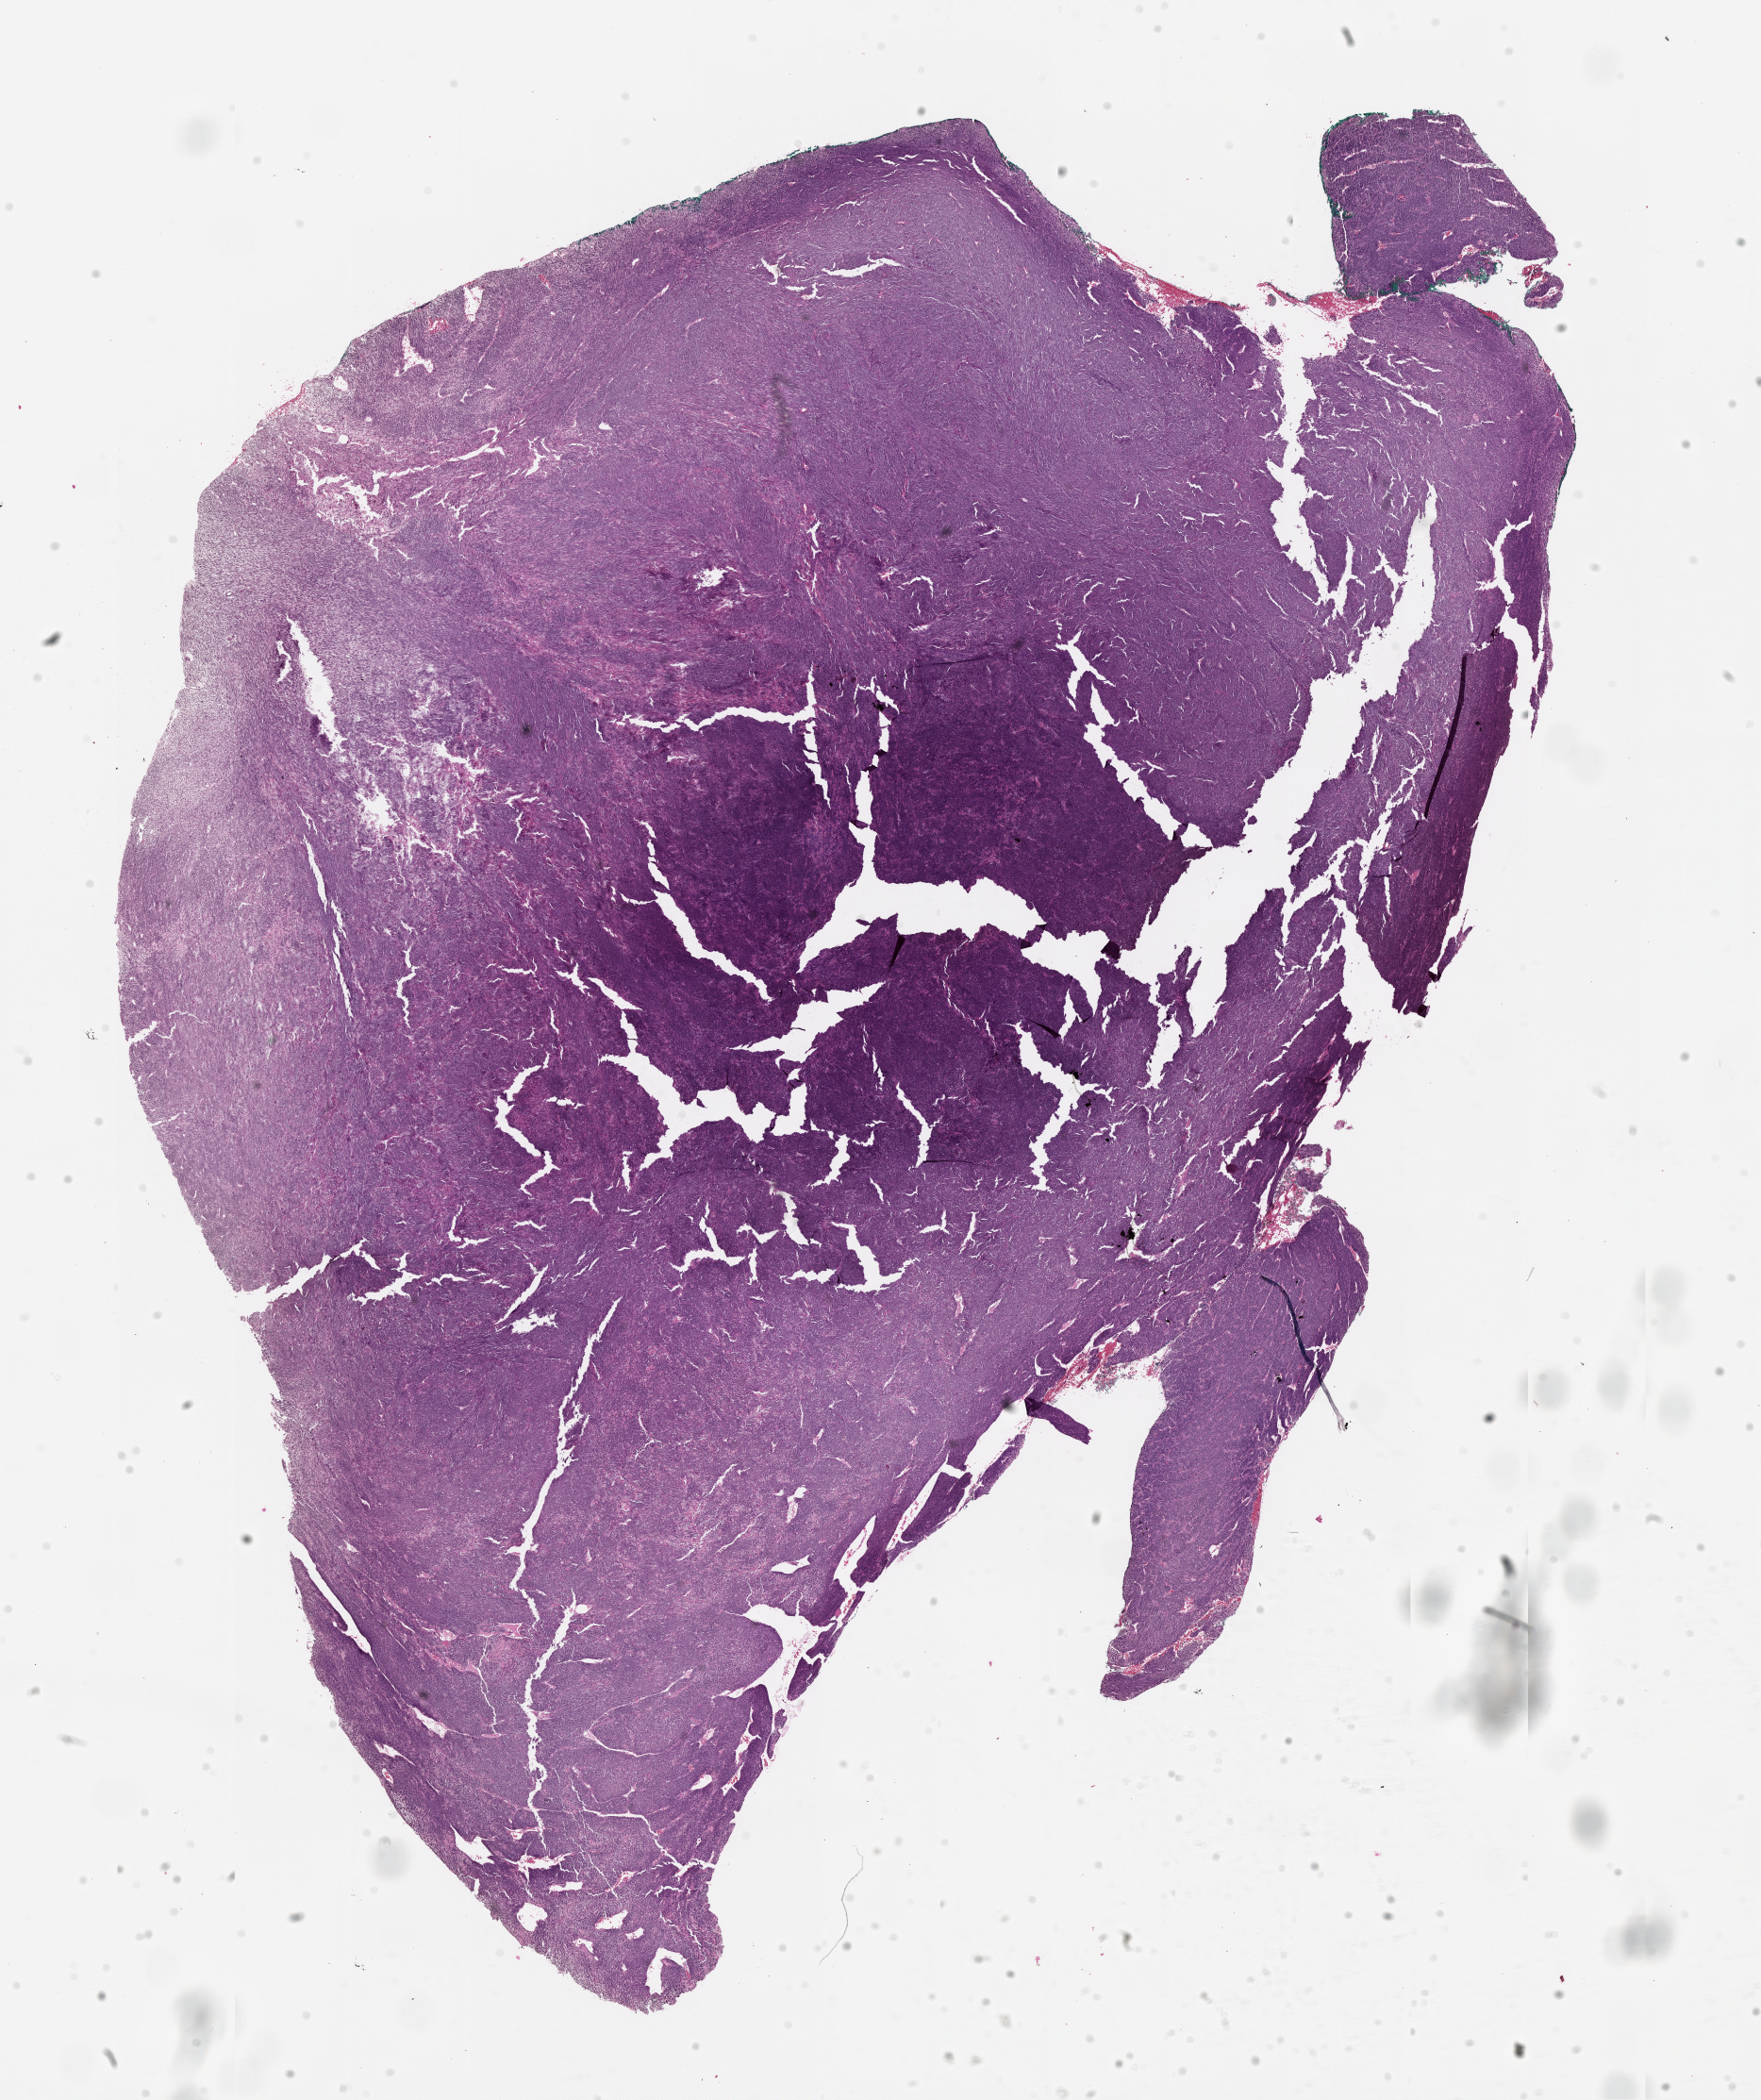
Hematoxylin and eosin (H&E) stained whole-slide image, shown as a low-resolution overview of the whole scanned area (about 15.0 x 17.9 mm, slide scanned at 20x).
Patient diagnosis (cohort enrolment): sarcoma (site not recorded at cohort level).